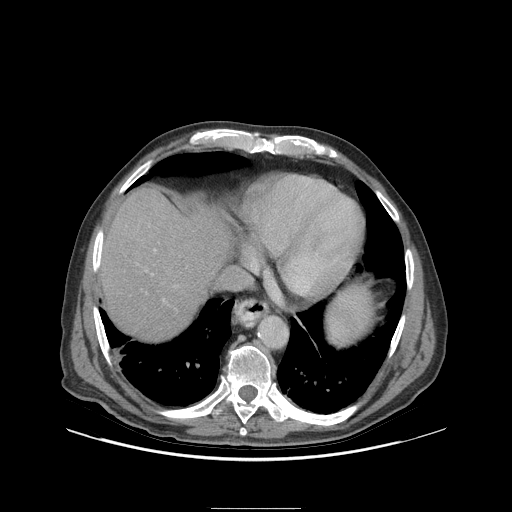
Contrast-enhanced abdominal CT (liver protocol), one axial slice. Slice 86 of 105 in the series (ordered by position). Reconstruction kernel STANDARD. 140 kVp. Soft-tissue window (W 400 / L 40 HU). 2.5 mm slice thickness. 512 × 512 image matrix. From the clinical record (not read from this slice): diagnosis: hepatocellular carcinoma (patient treated with transarterial chemoembolisation; whether this scan precedes or follows treatment is not stated here); TNM stage (as recorded): Stage-I; Child-Pugh class: A; tumour nodularity: uninodular.
Outlined on this slice (semi-automatically segmented with operator editing):
- liver parenchyma outside the tumour (the mass and vessels are separate outlines, so this box may not span the whole liver): bounding box [x1, y1, x2, y2] px = [98, 186, 230, 340]
- liver vessels: [151, 249, 155, 275]